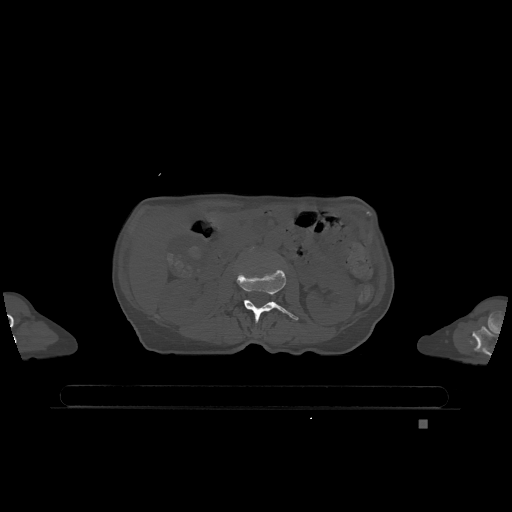
CT including the spine, one axial slice. Position 409 of 1317 along the scan axis. Bone window (W 1800 / L 400 HU). 0.5 mm slice thickness. 512 × 512 image matrix, field of view 500 × 500 mm. Patient: female, 74 years. From the clinical record (not read from this slice): primary cancer: lung; vertebrae with lytic lesions (as recorded): T1, T4, T5, T6, L4, L5.
Outlined on this slice (semi-automatically segmented with operator editing):
- L2 vertebra: bounding box [x1, y1, x2, y2] px = [237, 268, 299, 323]